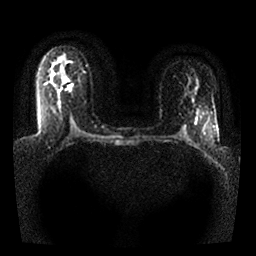
Breast MRI, one axial slice. Slice 18 of 25 in the series (ordered by position). Diffusion-weighted series; image 2 of 4 stored at this slice position (different b-values; order by instance number). 1.5 T. 4 mm slice thickness. 256 × 256 image matrix, field of view 330 × 330 mm. Female patient.
Annotated regions visible in this slice (expert manual segmentation):
- tumour on diffusion-weighted imaging: bounding box [x1, y1, x2, y2] px = [68, 85, 73, 91]